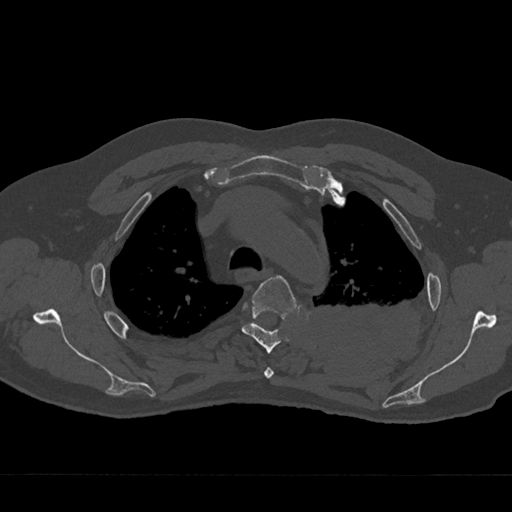
CT including the spine, one axial slice. Position 525 of 797 along the scan axis. Reconstruction kernel Br40s/3. 120 kVp. Bone window (W 1800 / L 400 HU). 512 × 512 image matrix, field of view 377 × 377 mm. Male patient, age 75 years. From the clinical record (not read from this slice): primary cancer: renal.
Annotated regions visible in this slice (semi-automatic segmentation, software-assisted and operator-edited):
- T3 vertebra: bounding box <264,367,274,379> (left, top, right, bottom; pixels)
- T4 vertebra: <241,275,296,354>